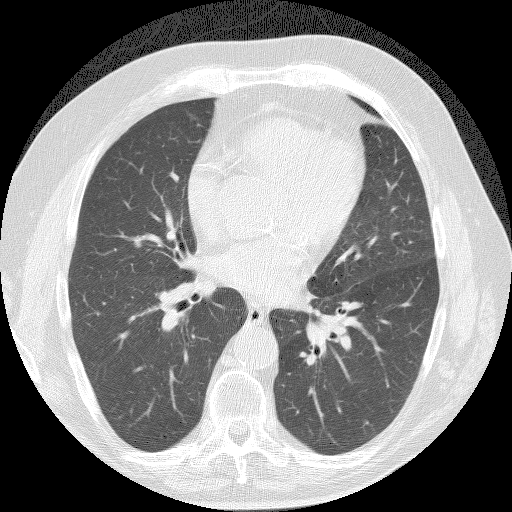
Low-dose screening chest CT, axial slice, baseline screening round, lung window (W 1500 / L -600 HU), 2.5 mm slice thickness, slice 82 of 145 in the series, 512 × 512 image matrix. Male participant, aged 61 years at enrolment. Current smoker at enrolment.
- Expert-annotated lung lesion, bounding box [x1, y1, x2, y2] px = [107, 224, 155, 264].
- The screening reader recorded 3 non-calcified nodules or masses ≥4 mm on this exam (right upper lobe, right lower lobe); which of them this box marks is not recorded.
- Participant outcome: lung cancer diagnosed 491 days after this screen (after the second annual screen) — bronchiolo-alveolar adenocarcinoma, NOS, right middle lobe, well differentiated (G1), stage IA (AJCC 6th edition), 15 mm at pathology.